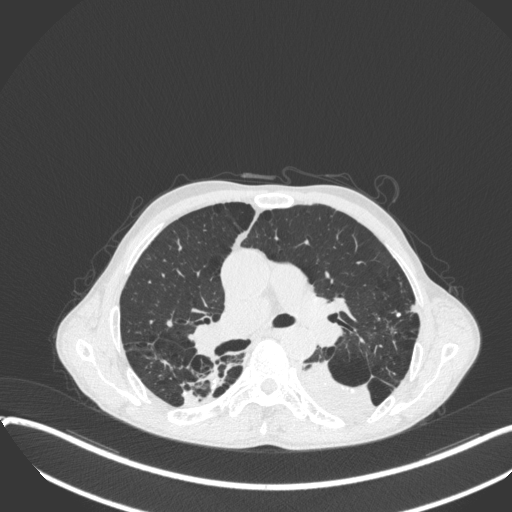
Chest CT, one axial slice; slice 232 of 400 in the series (ordered by position); reconstruction kernel B31f; lung window (W 1500 / L -600 HU); 1 mm slice thickness; 512 × 512 image matrix, field of view 400 × 400 mm. Male patient, age 57 years. Case-level facts recorded for this patient, not image findings: clinical TNM (as recorded): T4 N0 M0.
Annotated regions visible in this slice (rectangle marked by the reading radiologist):
- lung tumour (recorded histology: squamous cell carcinoma): bounding box <299,359,376,418> (left, top, right, bottom; pixels)